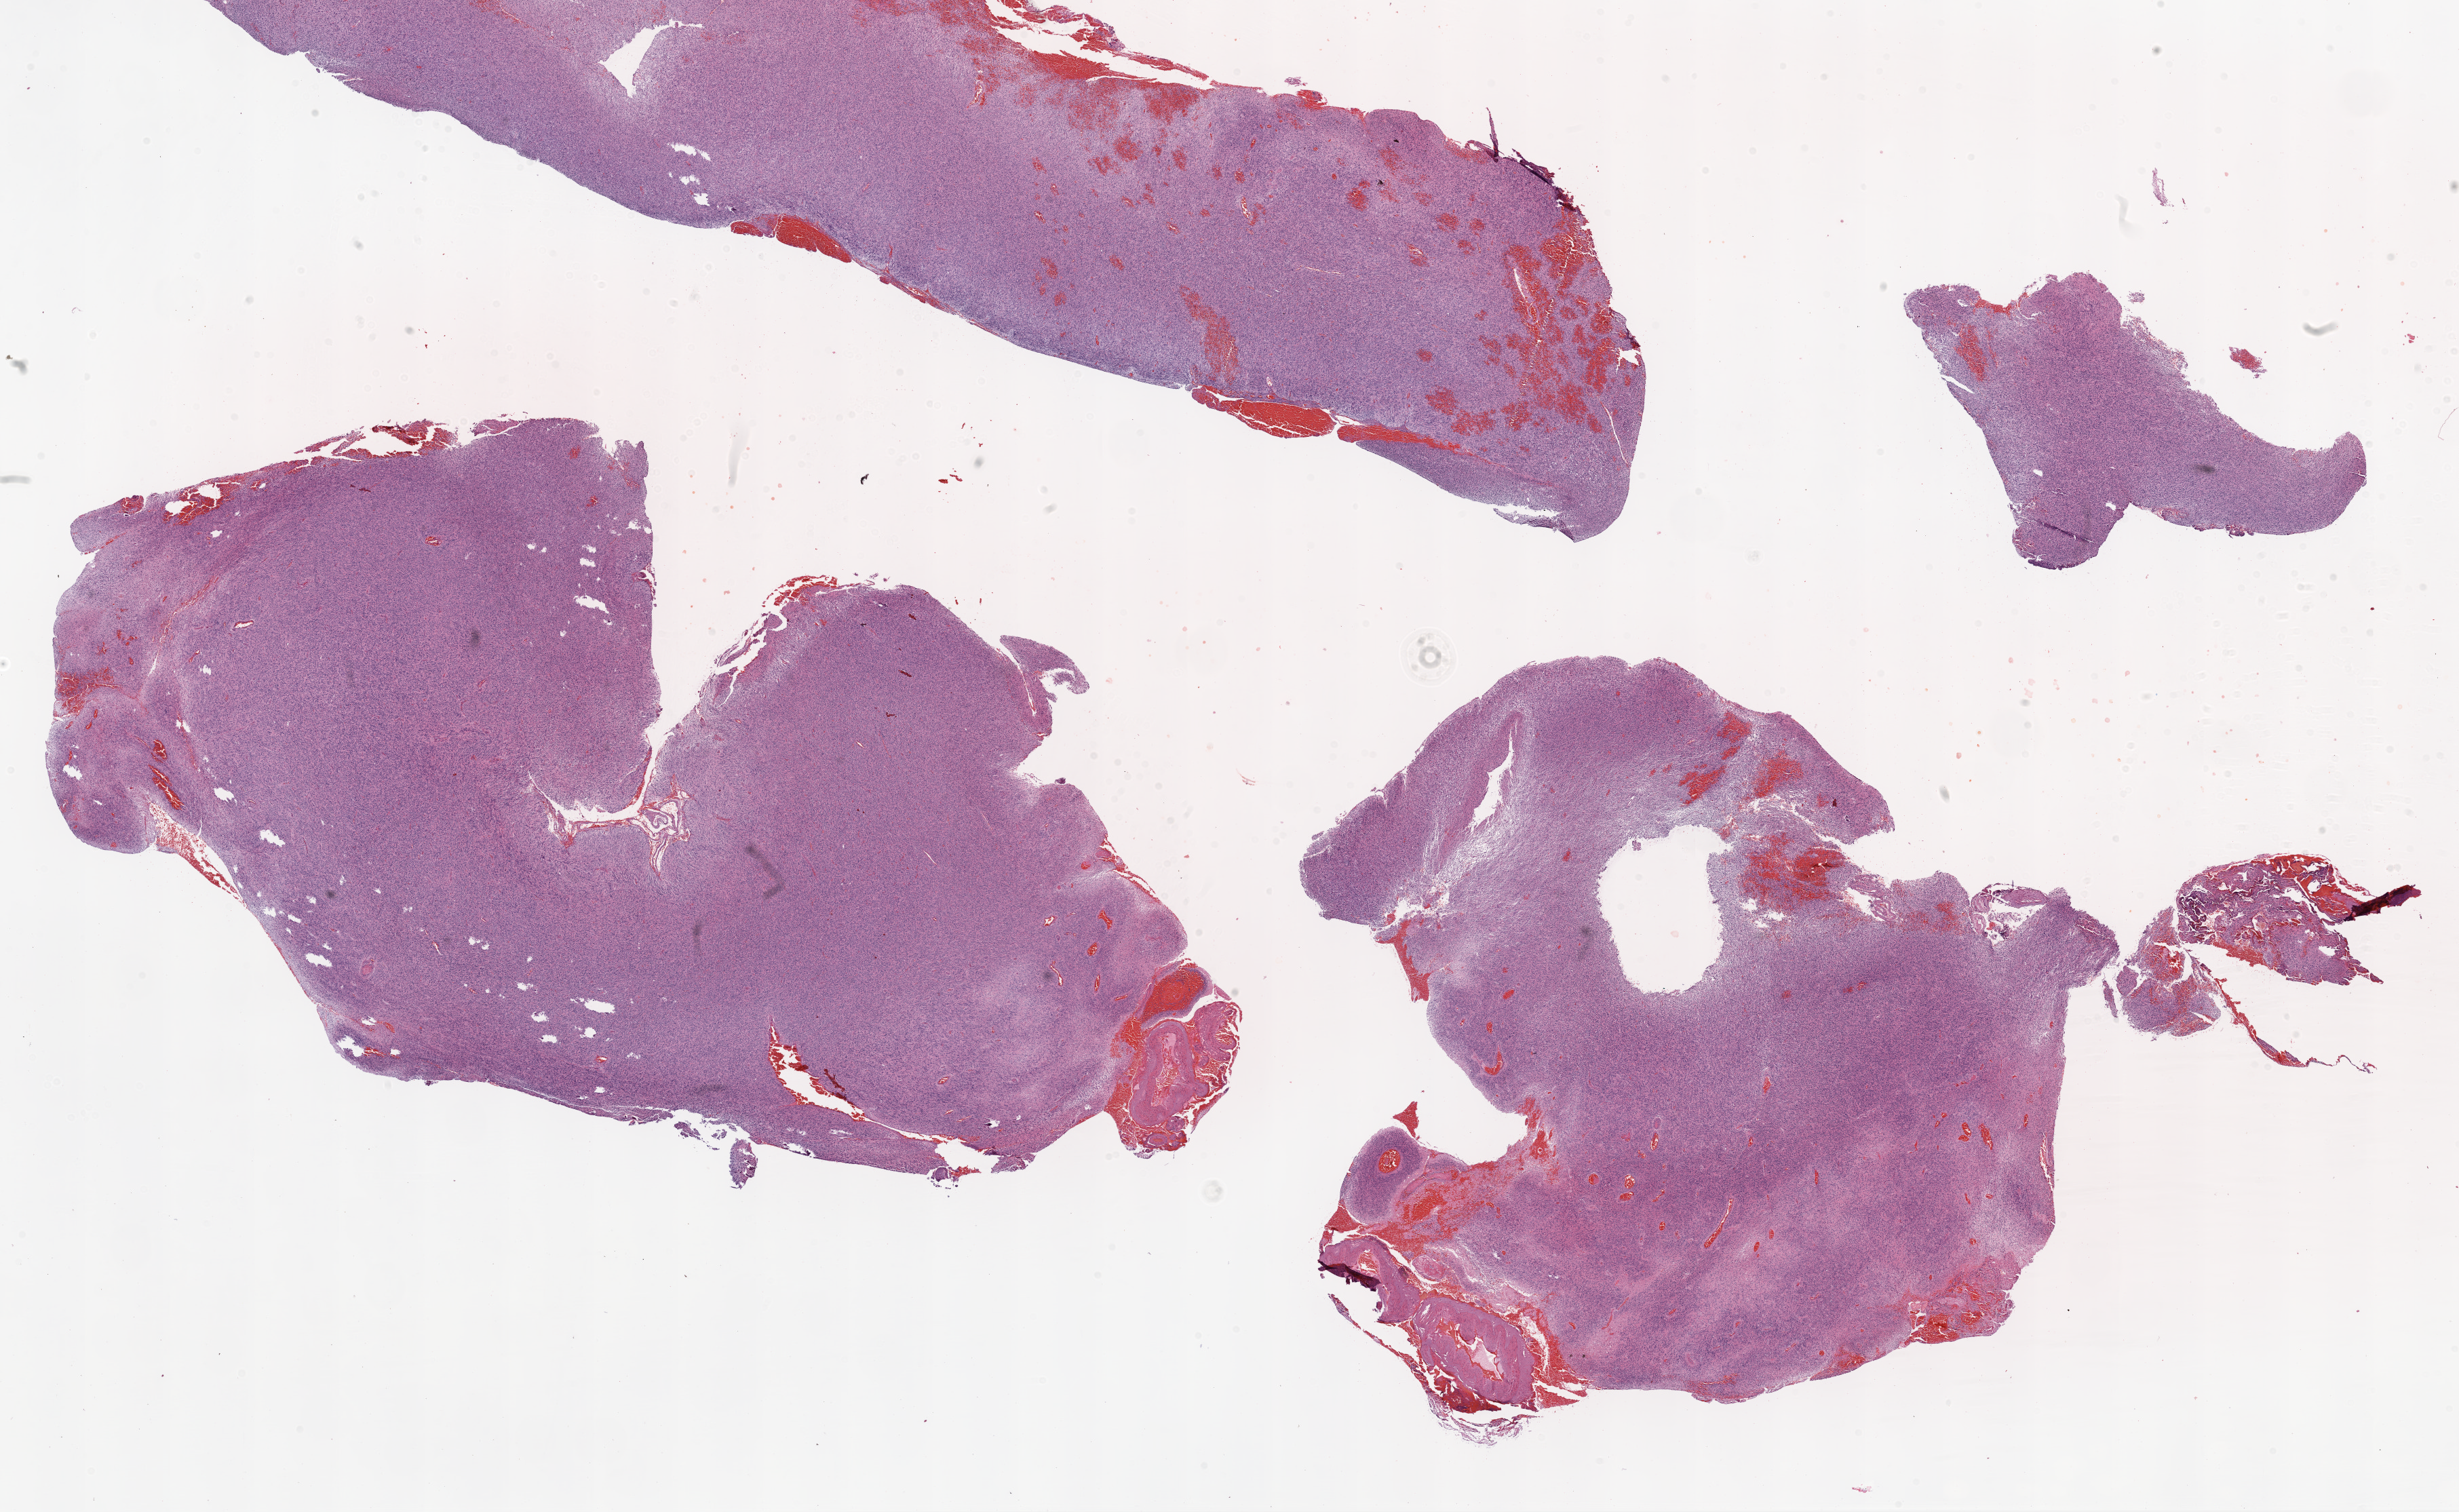
Whole-slide histology image, H&E — whole scanned area (about 29.1 x 17.9 mm, acquisition: 20x scan) shown as a low-resolution overview; FFPE section; primary tumour sample from the brain. Male, age 53 years at initial diagnosis.
Pathologic diagnosis: Glioblastoma.